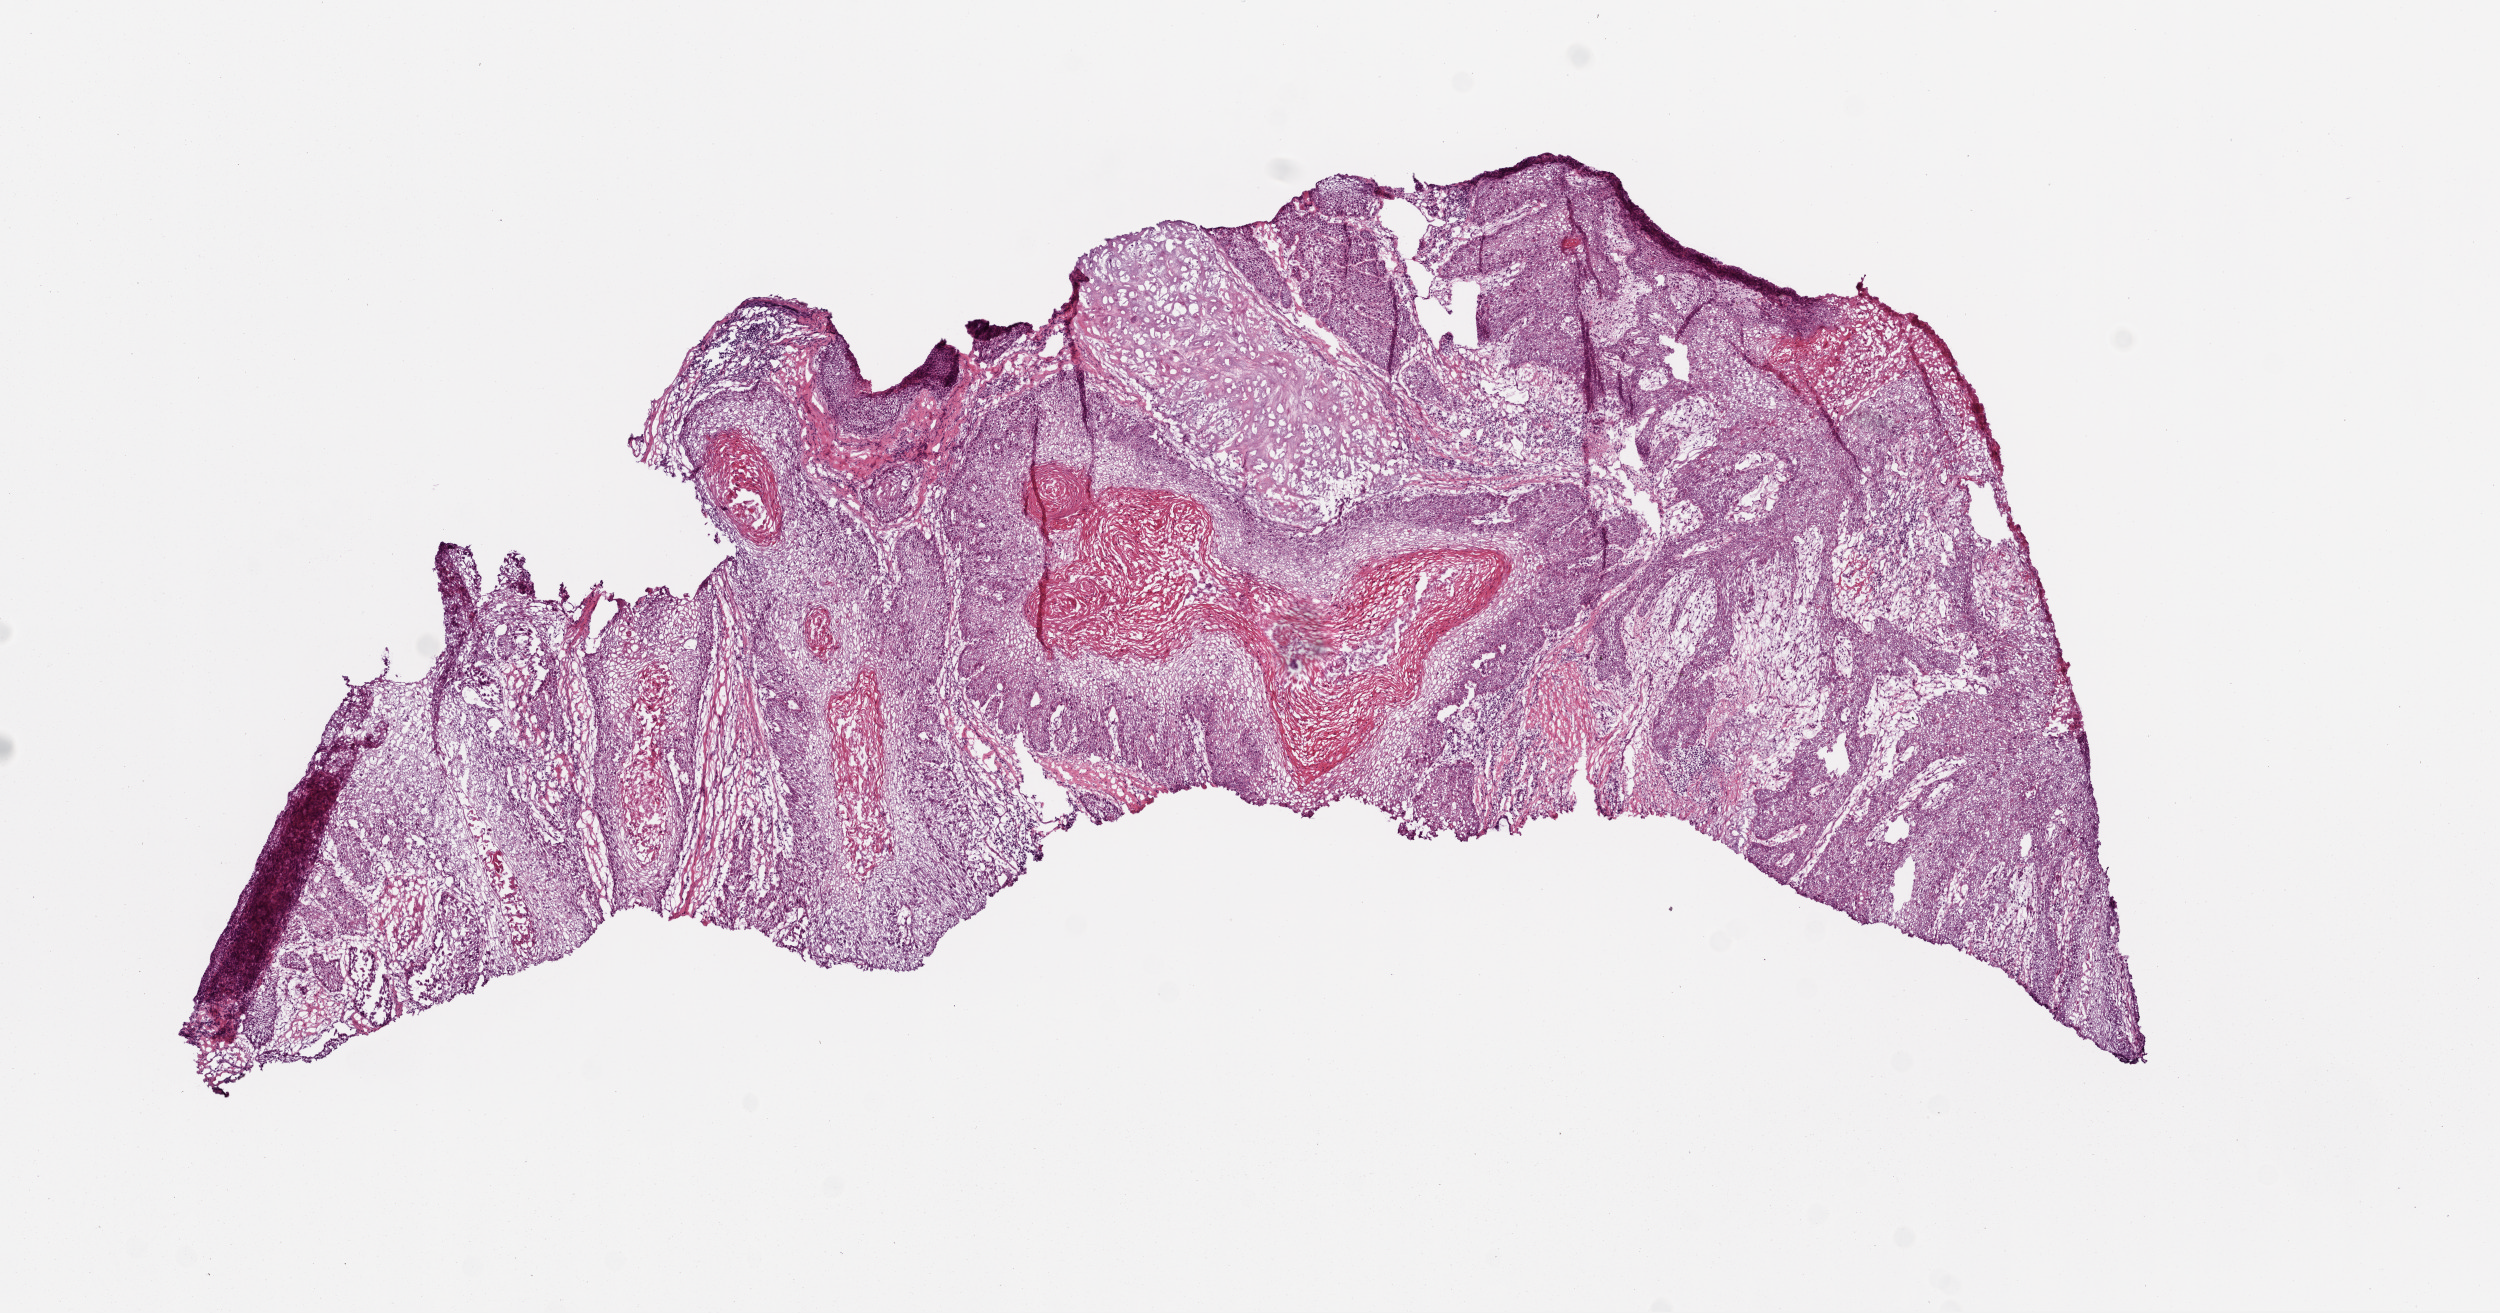
Whole-slide histology image, Hematoxylin and eosin (H&E) stained — whole scanned area (about 10.0 x 5.3 mm) shown as a low-resolution overview; frozen section from the top of the tissue portion; head and neck, primary tumour sample. Male, age 56 years at initial diagnosis.
Pathologic diagnosis: Squamous cell carcinoma, NOS.